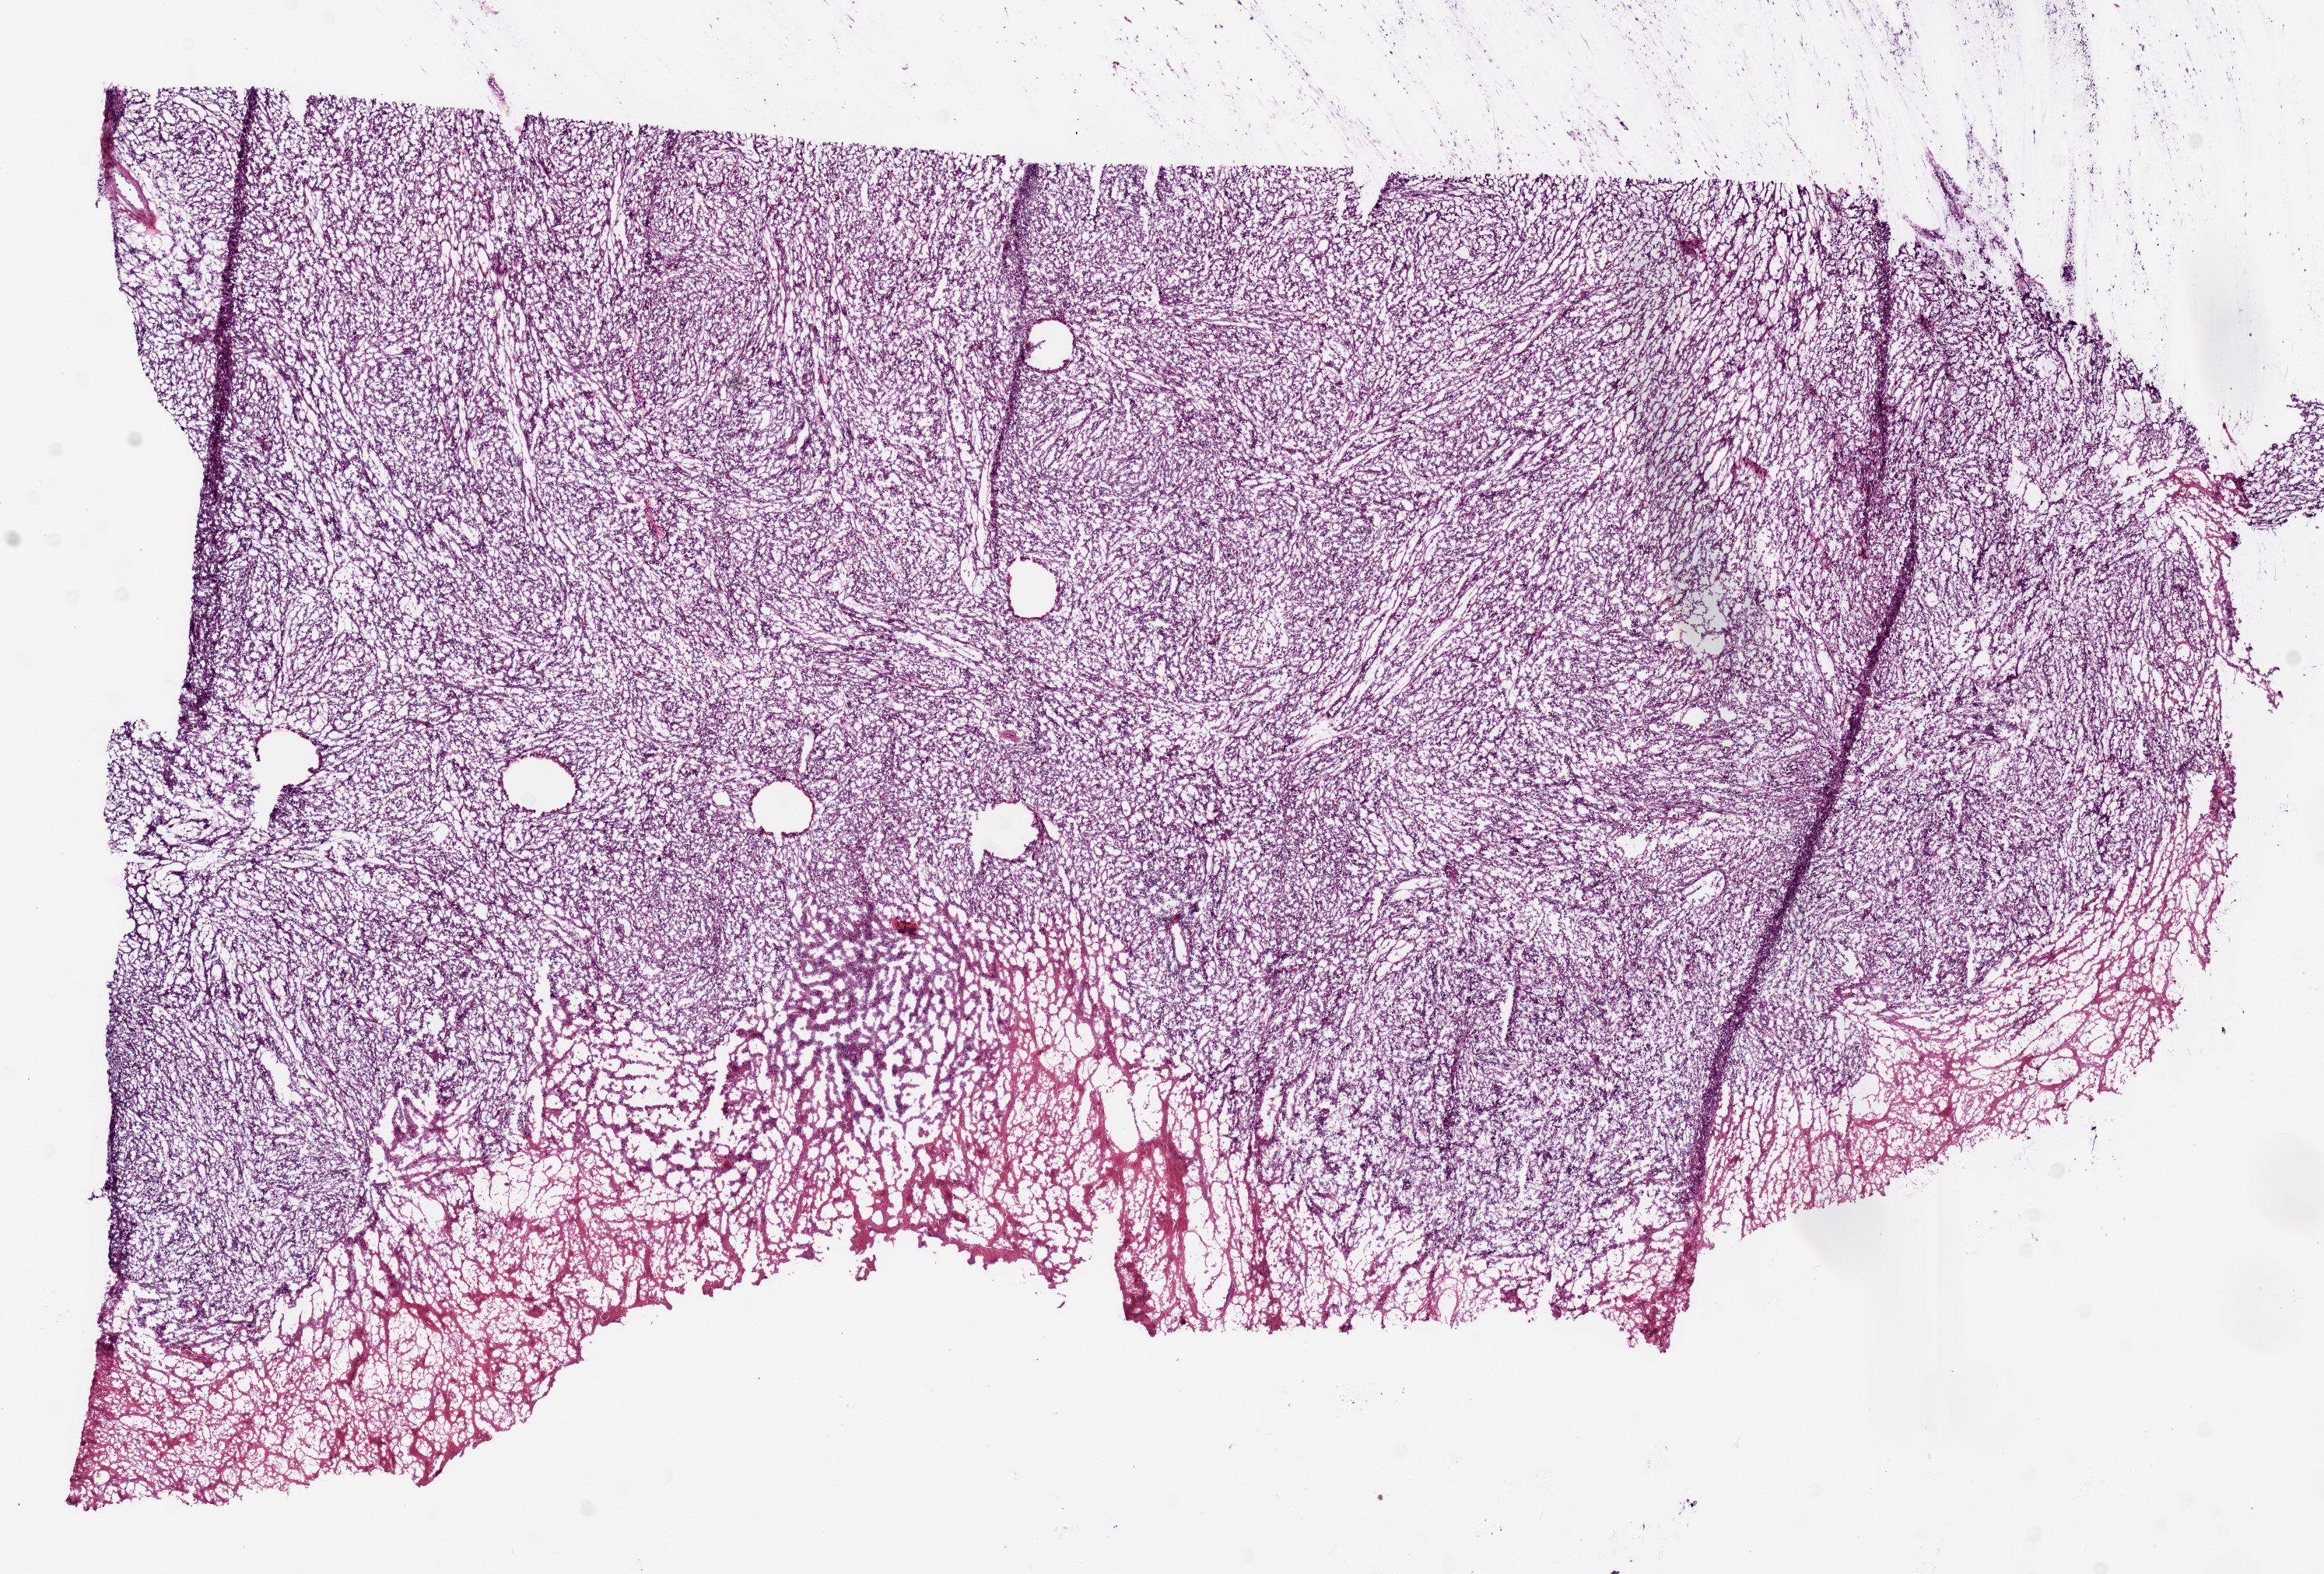
Digitized Hematoxylin and eosin (H&E) stained tissue section (whole slide) — a low-resolution overview of the entire scanned area, about 11.8 x 8.0 mm (acquisition: 20x scan). Frozen section. Primary tumour sample from the cervix. Patient: female, age at initial diagnosis 40 years. Histologic grade: G3 (poorly differentiated). Pathologist review of this section (percent, as recorded): tumour cells 85%, tumour nuclei 60%, normal cells 0%, stromal cells 15%, necrosis 0%. Infiltration values recorded for this section: lymphocyte infiltration 0%, monocyte infiltration 0%, neutrophil infiltration 0%.
- lymph nodes positive (case pathology): 0 of 12 examined
- pathologic diagnosis: Squamous cell carcinoma, NOS
- FIGO stage: IB